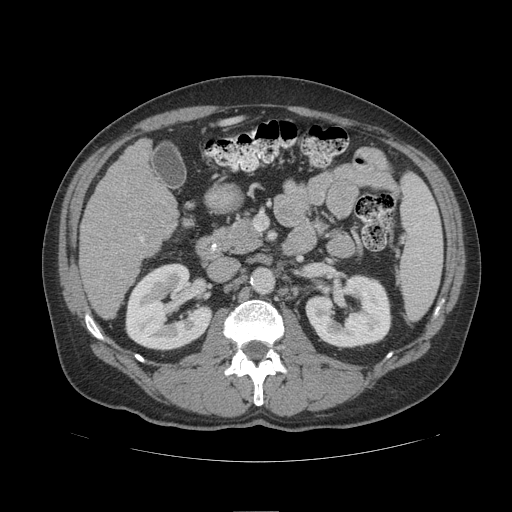
Contrast-enhanced abdominal CT (liver protocol), one axial slice. Position 47 of 109 along the scan axis. Reconstruction kernel STANDARD. 140 kVp. Soft-tissue window (W 400 / L 40 HU). 2.5 mm slice thickness. 512 × 512 image matrix. From the clinical record (not read from this slice): diagnosis: hepatocellular carcinoma (patient treated with transarterial chemoembolisation; whether this scan precedes or follows treatment is not stated here); TNM stage (as recorded): Stage-IIIB; Child-Pugh class: A; tumour nodularity: multinodular.
Structures marked on this image (semi-automatic segmentation, software-assisted and operator-edited):
- liver parenchyma outside the tumour (the mass and vessels are separate outlines, so this box may not span the whole liver): bounding box [x1, y1, x2, y2] px = [80, 138, 178, 318]
- liver vessels: [140, 237, 144, 241]